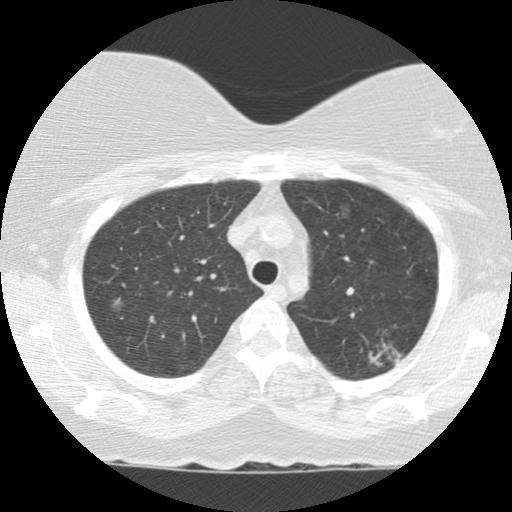
Chest CT (low-dose screening protocol), one axial image, first (baseline) screen, lung window (W 1500 / L -600 HU), standard (soft-tissue) reconstruction kernel (STANDARD), slice 25 of 123 in the series, 512 × 512 image matrix. Female participant, aged 56 years at enrolment. Current smoker at enrolment.
- Expert-annotated lung lesion, bounding box <356,318,418,383> (left, top, right, bottom; pixels).
- The screening reader recorded 4 non-calcified nodules or masses ≥4 mm on this exam; which of them this box marks is not recorded.
- Official screen result: positive, change unspecified: nodule(s) >= 4 mm or enlarging nodule(s), mass(es), or other non-specific abnormalities suspicious for lung cancer.